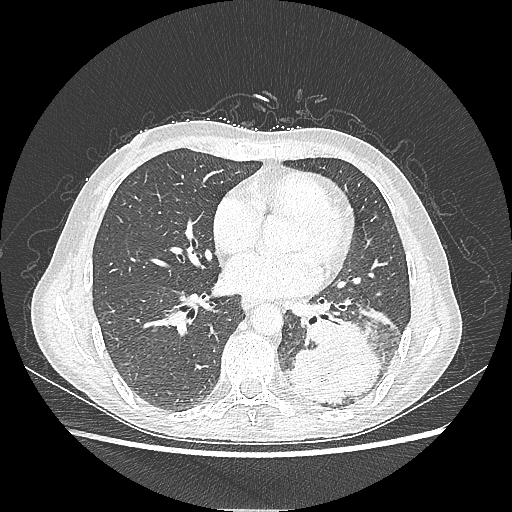
Chest CT, one axial slice; slice 99 of 220 in the series (ordered by position); reconstruction kernel LUNG; 80 kVp; lung window (W 1500 / L -600 HU); 1.25 mm slice thickness; 512 × 512 image matrix, field of view 360 × 360 mm. Female patient, age 53 years. From the clinical record (not read from this slice): clinical TNM (as recorded): T3 N0 M0.
Structures marked on this image (bounding box drawn by a radiologist):
- lung tumour (recorded histology: adenocarcinoma): bounding box (x1, y1, x2, y2) in pixels: (285, 316, 382, 406)